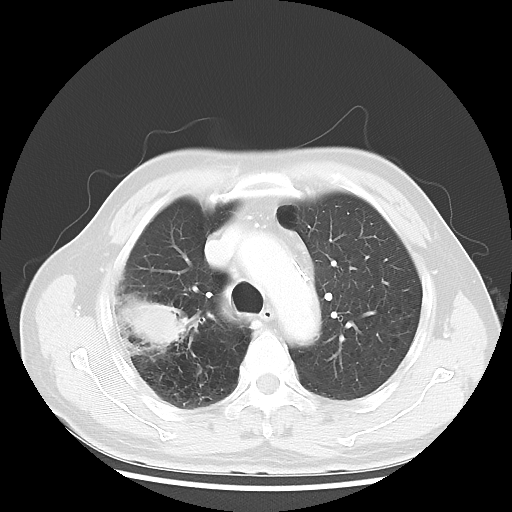
Chest CT, one axial slice; position 37 of 50 along the scan axis; reconstruction kernel LUNG; 120 kVp; lung window (W 1500 / L -600 HU); 512 × 512 image matrix, field of view 360 × 360 mm. Patient: male, 69 years. Case-level facts recorded for this patient, not image findings: clinical TNM (as recorded): T3 N0 M0.
Annotated regions visible in this slice (rectangle marked by the reading radiologist):
- lung tumour (recorded histology: adenocarcinoma): box from (x=115, y=288) to (x=200, y=358) px